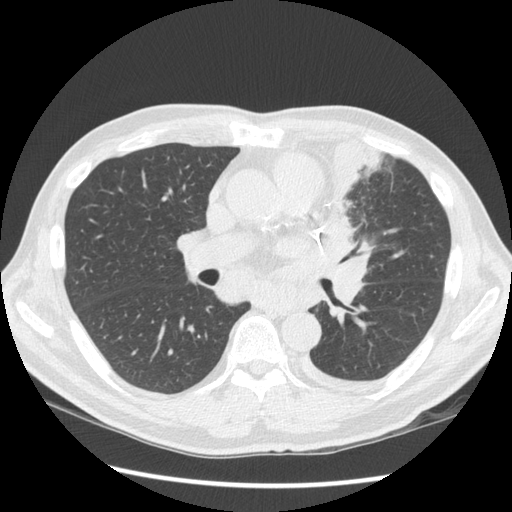
Low-dose screening chest CT, one axial slice. Slice 79 of 136 in the series (ordered by position). Reconstruction kernel STANDARD. 120 kVp. Lung window (W 1500 / L -600 HU). 2.5 mm slice thickness. 512 × 512 image matrix, field of view 360 × 360 mm.
Outlined on this slice (manually delineated by an expert):
- lesion 1 (tumor, upper lobe of left lung): bounding box [x1, y1, x2, y2] px = [319, 139, 385, 261]